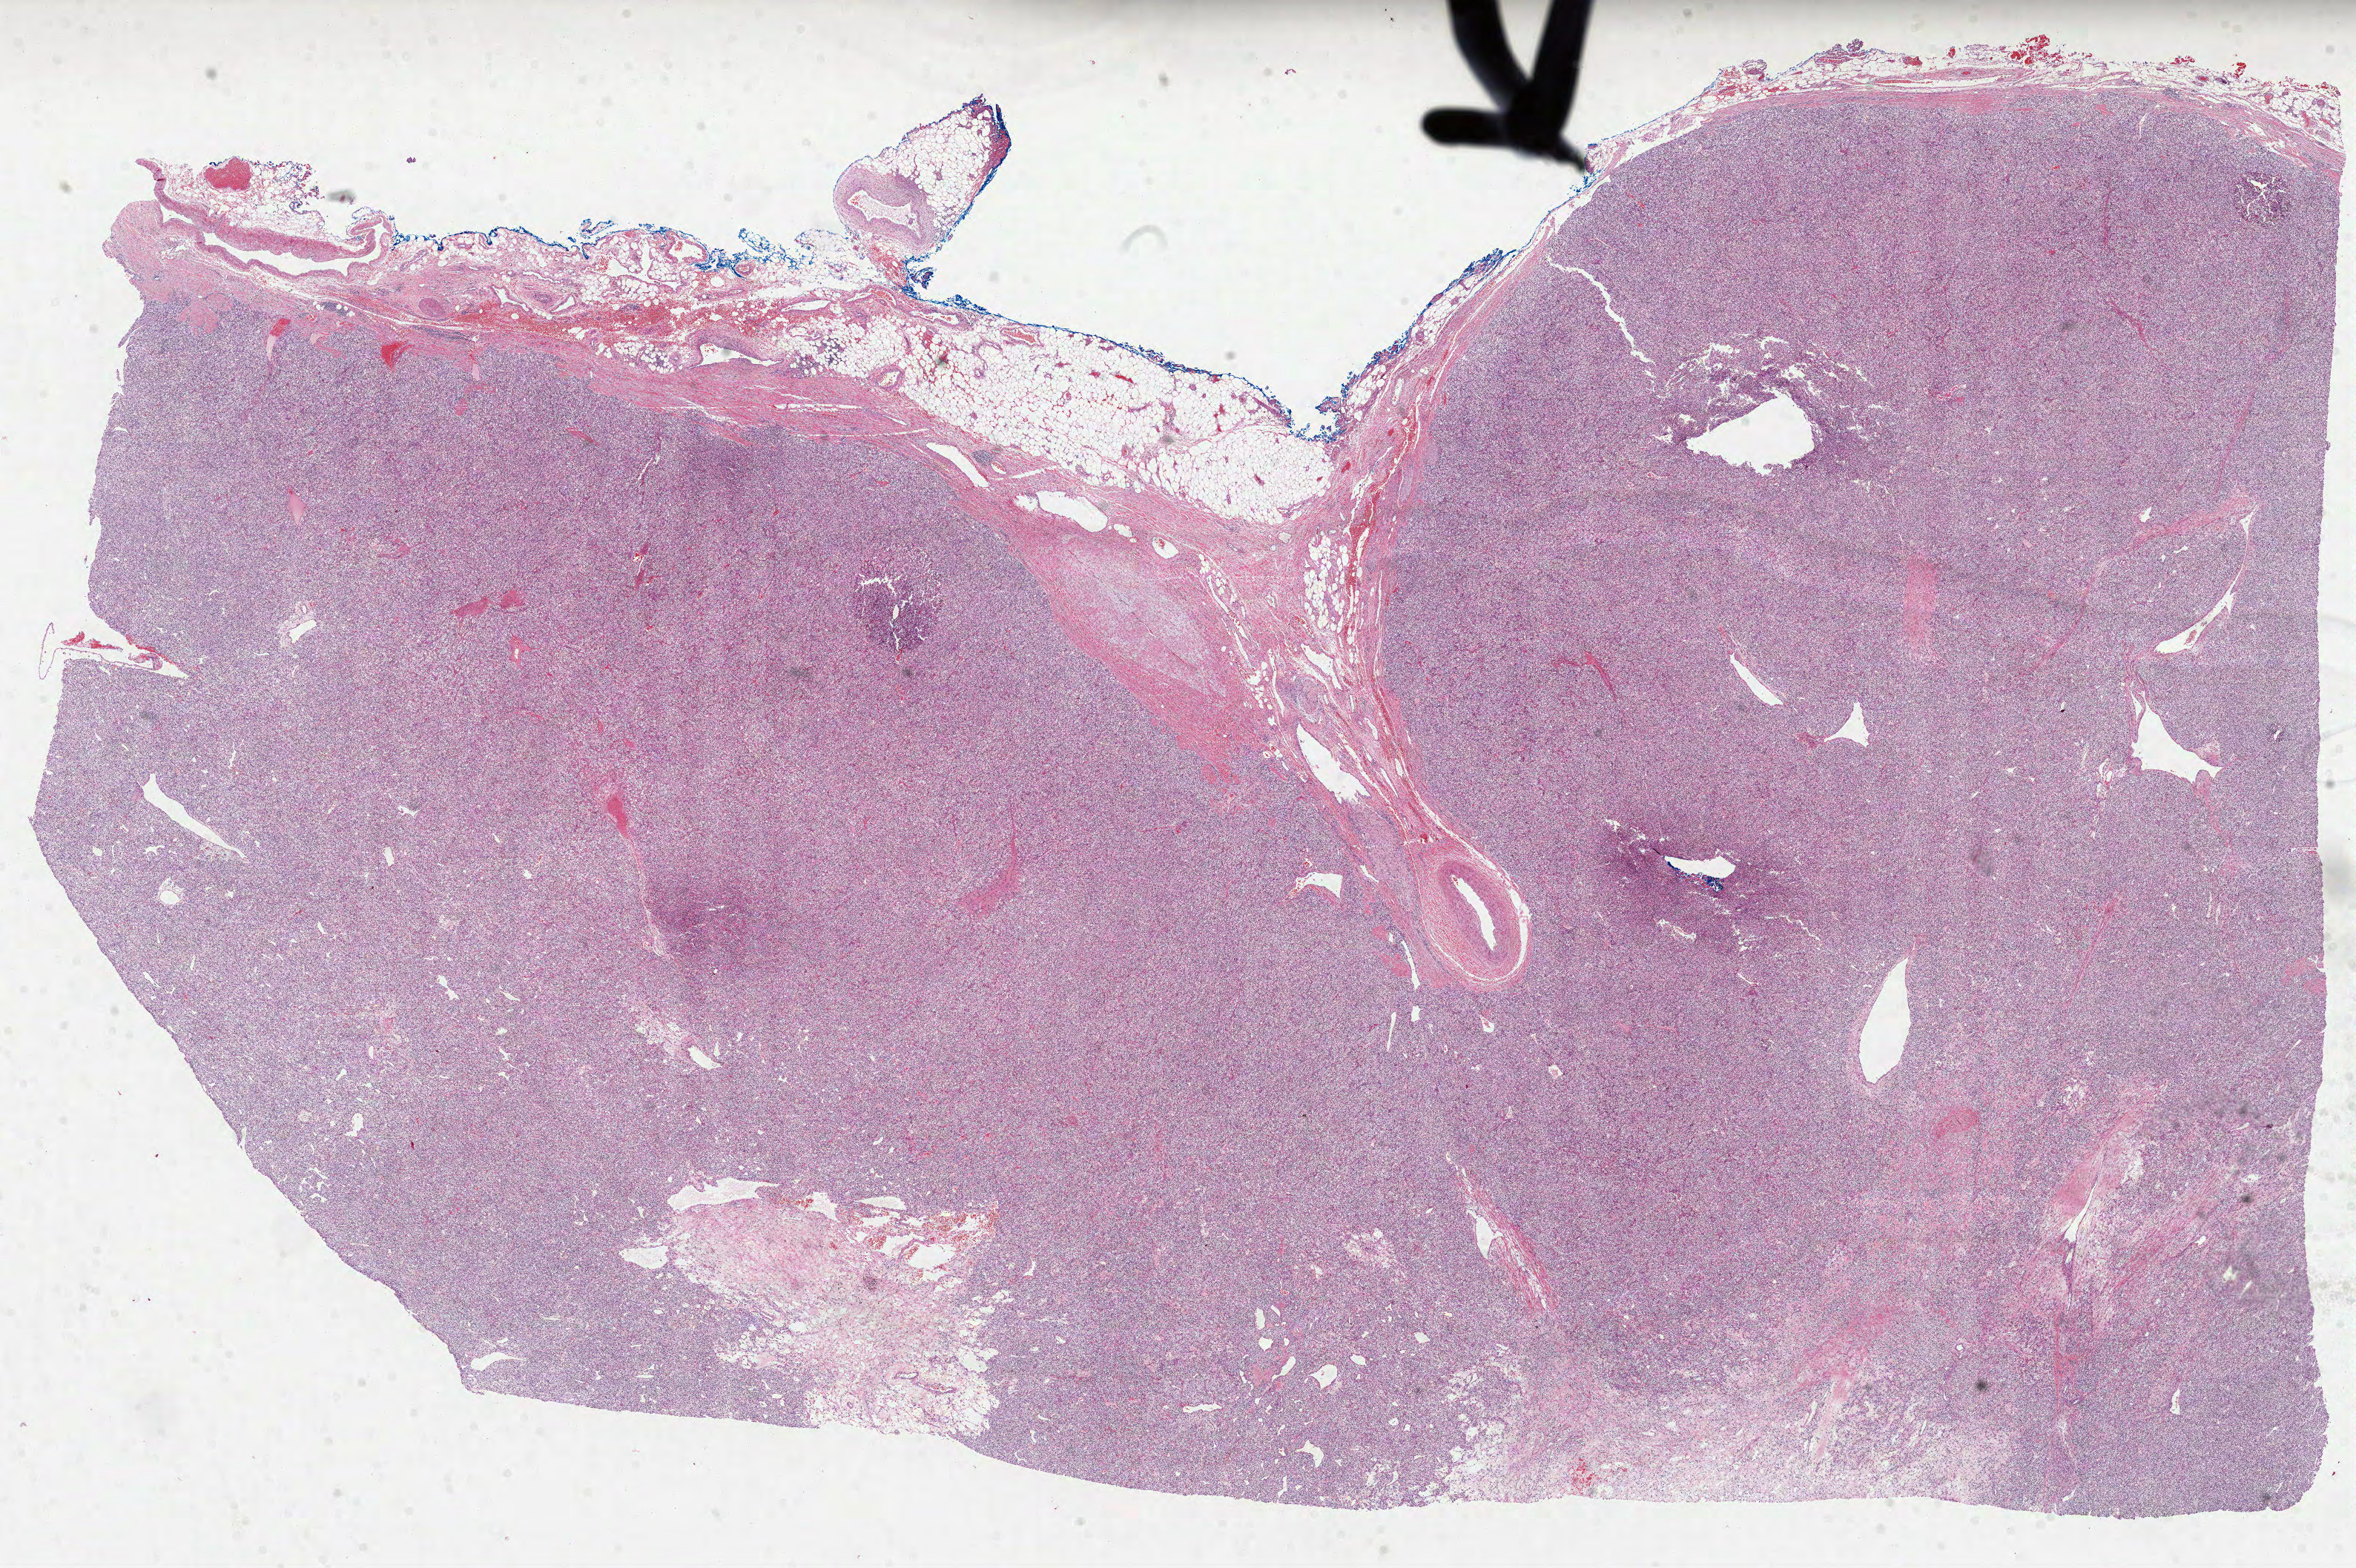
H&E-stained whole-slide image — low-resolution overview of the scanned area, about 25.6 x 17.1 mm. FFPE section. Kidney, primary tumour sample. Male patient; age at initial diagnosis 70 years. Histologic grade: G2 (moderately differentiated).
- TNM: T3a NX M1
- diagnosis: Clear cell adenocarcinoma, NOS
- AJCC pathologic stage: IV (6th edition)